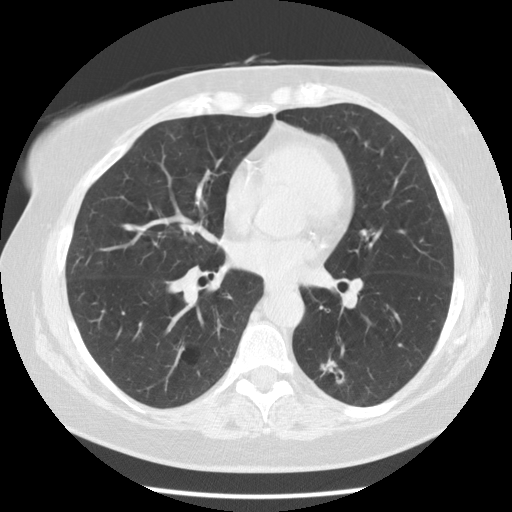
Axial slice from a low-dose chest CT screening exam. Second annual screen. Lung window (W 1500 / L -600 HU). 2.5 mm slice thickness. Standard (soft-tissue) reconstruction kernel (STANDARD). Slice 62 of 118 in the series. 512 × 512 image matrix. Female, age 59 years at enrolment.
Expert reader's lesion annotation, bounding box [x1, y1, x2, y2] px = [297, 342, 369, 408]. The screening reader recorded 5 non-calcified nodules or masses ≥4 mm on this exam; which of them this box marks is not recorded. Official screen result: positive, other. Lung cancer was diagnosed 343 days after this screen (after the third annual screen): adenocarcinoma, NOS, left lower lobe, poorly differentiated (G3), stage IA (AJCC 6th edition), 15 mm at pathology.